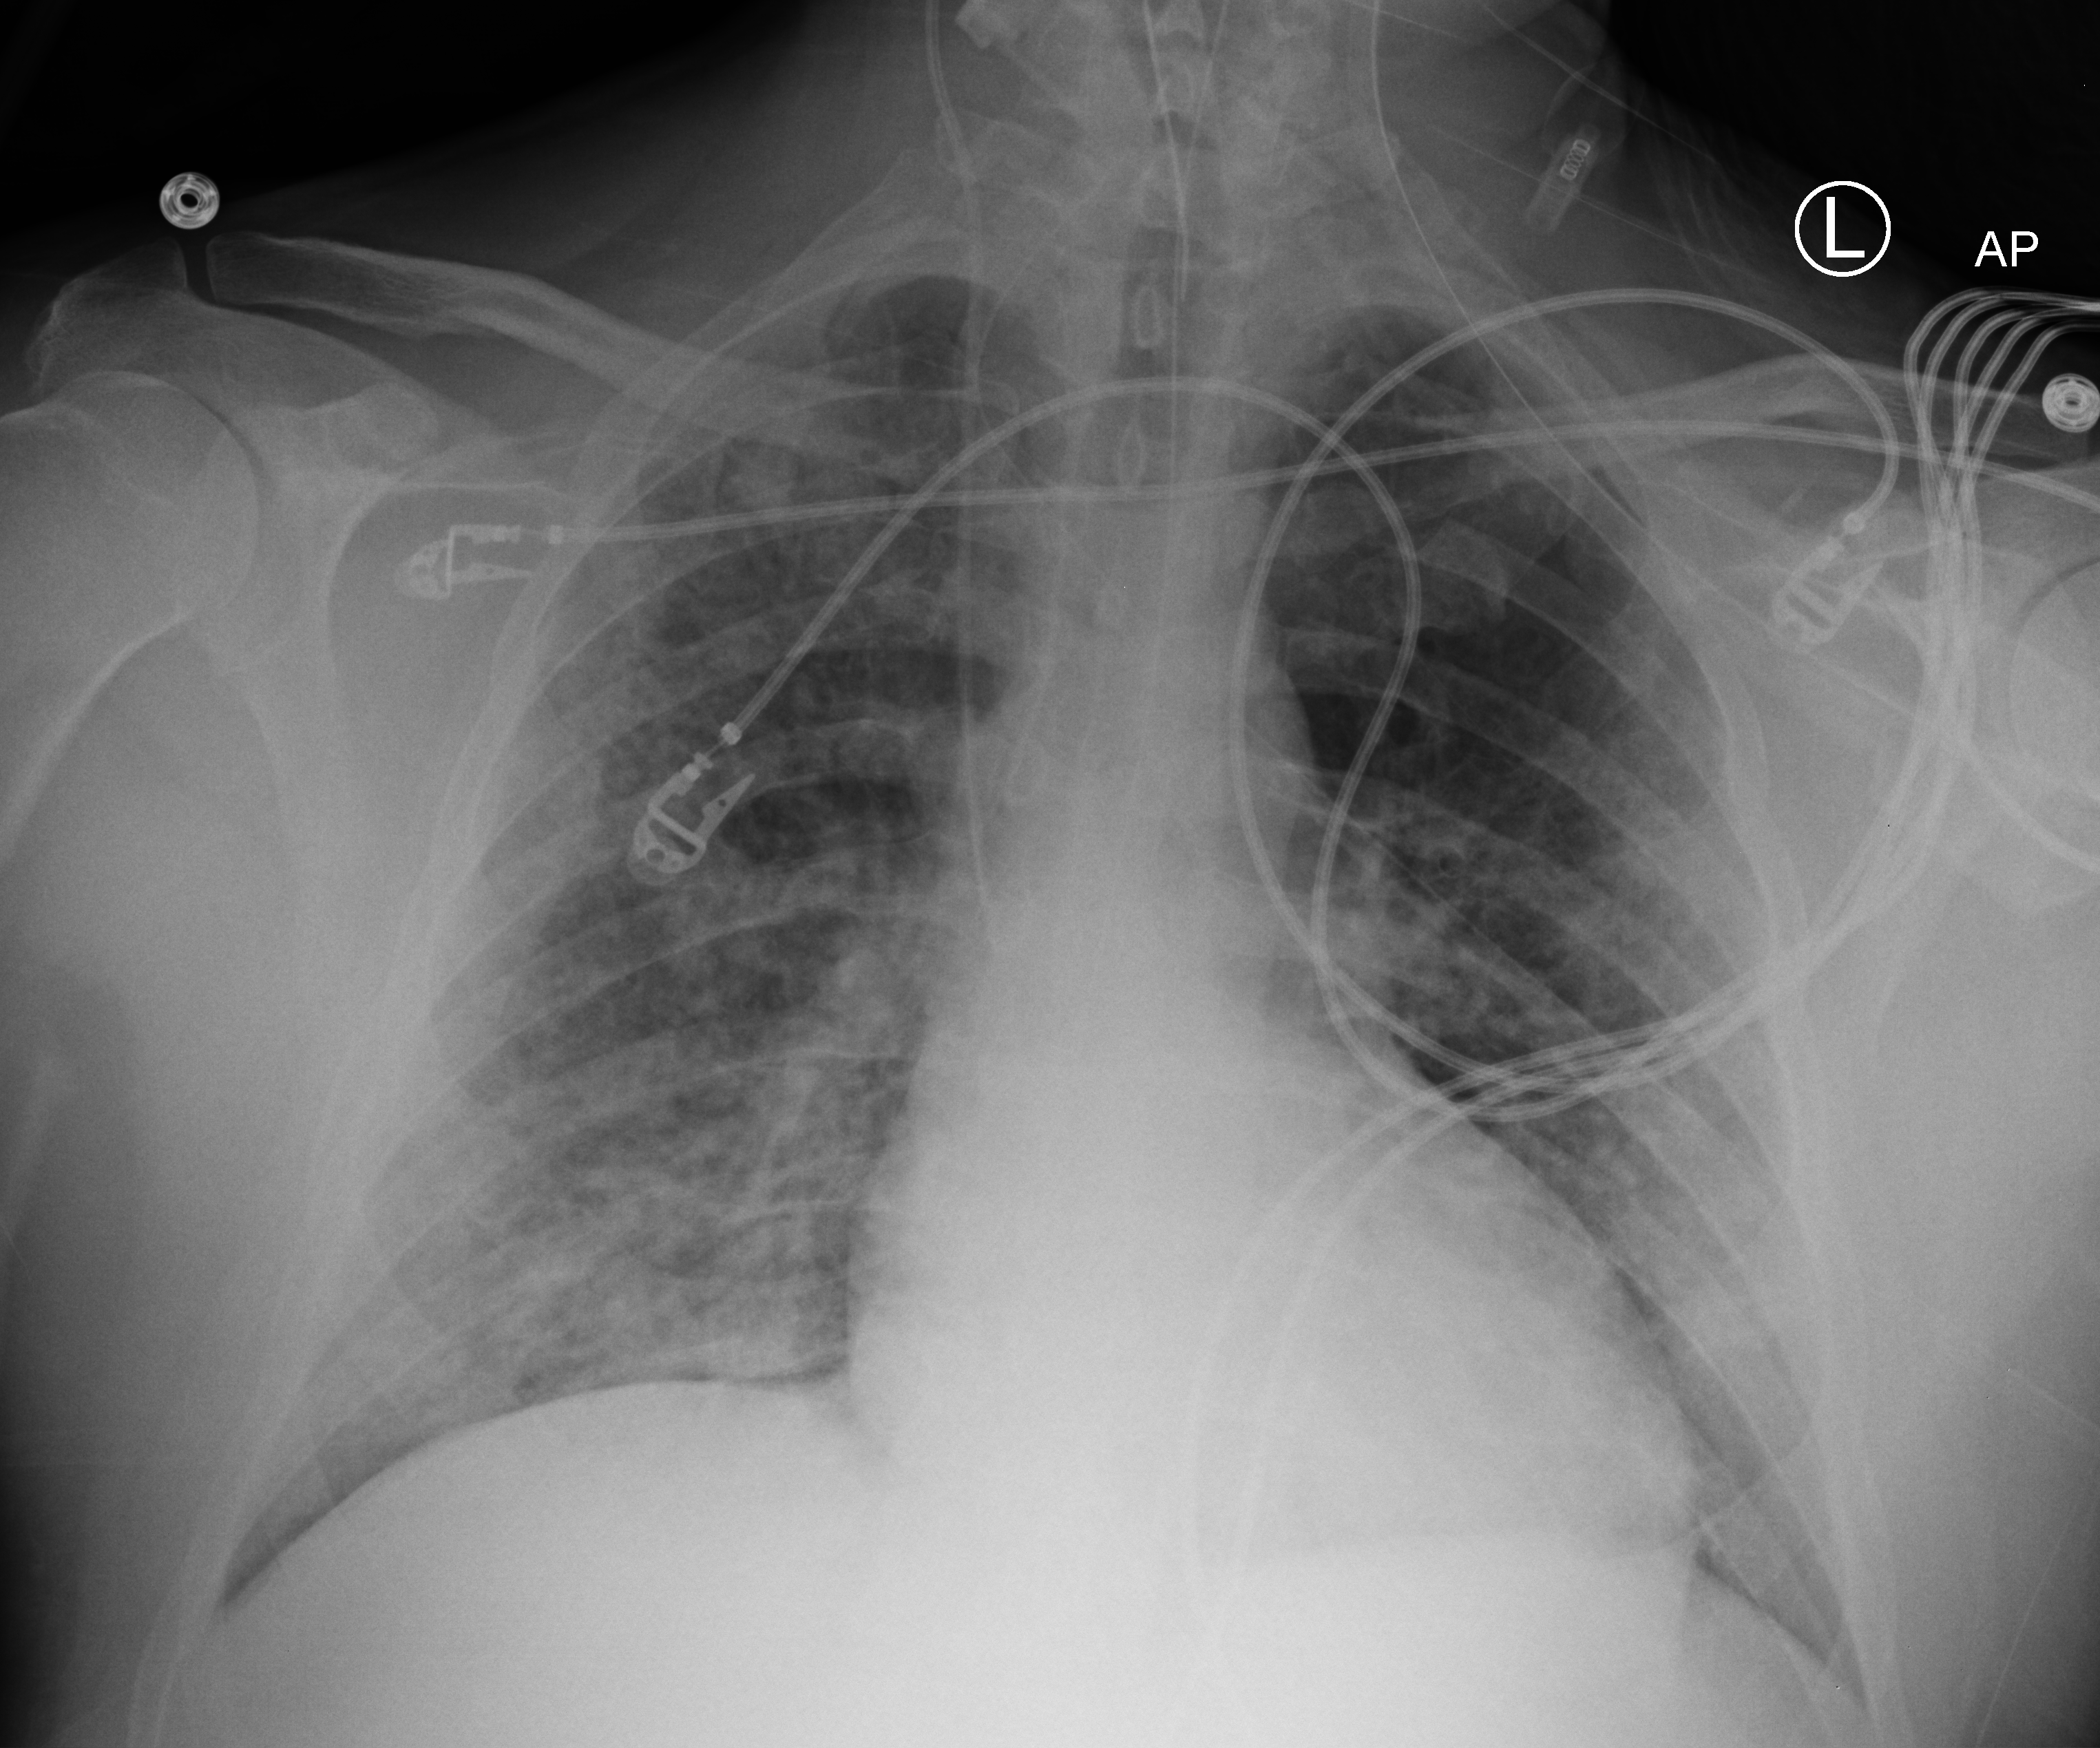
Chest X-ray (portable). Male patient hospitalised with COVID-19, age 18–59 years.
Admission-level facts for this patient (not findings on this image; timing relative to this image not recorded):
- mechanically ventilated during this hospital stay: yes
- admitted to intensive care during this hospital stay: no